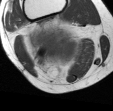
MRI of an extremity soft-tissue mass, one axial slice; position 34 of 45 along the scan axis; MR volume resampled by the dataset authors to the PET/CT grid (not the native acquisition matrix); 3.27 mm slice thickness; 113 × 111 image matrix. Female patient. Case-level facts recorded for this patient, not image findings: histological type: liposarcoma; site of the primary tumour: right thigh.
Outlined on this slice (expert contour drawn on MRI and transferred to this co-registered scan by the dataset authors):
- gross tumour volume (mass): box from (x=28, y=26) to (x=82, y=66) px